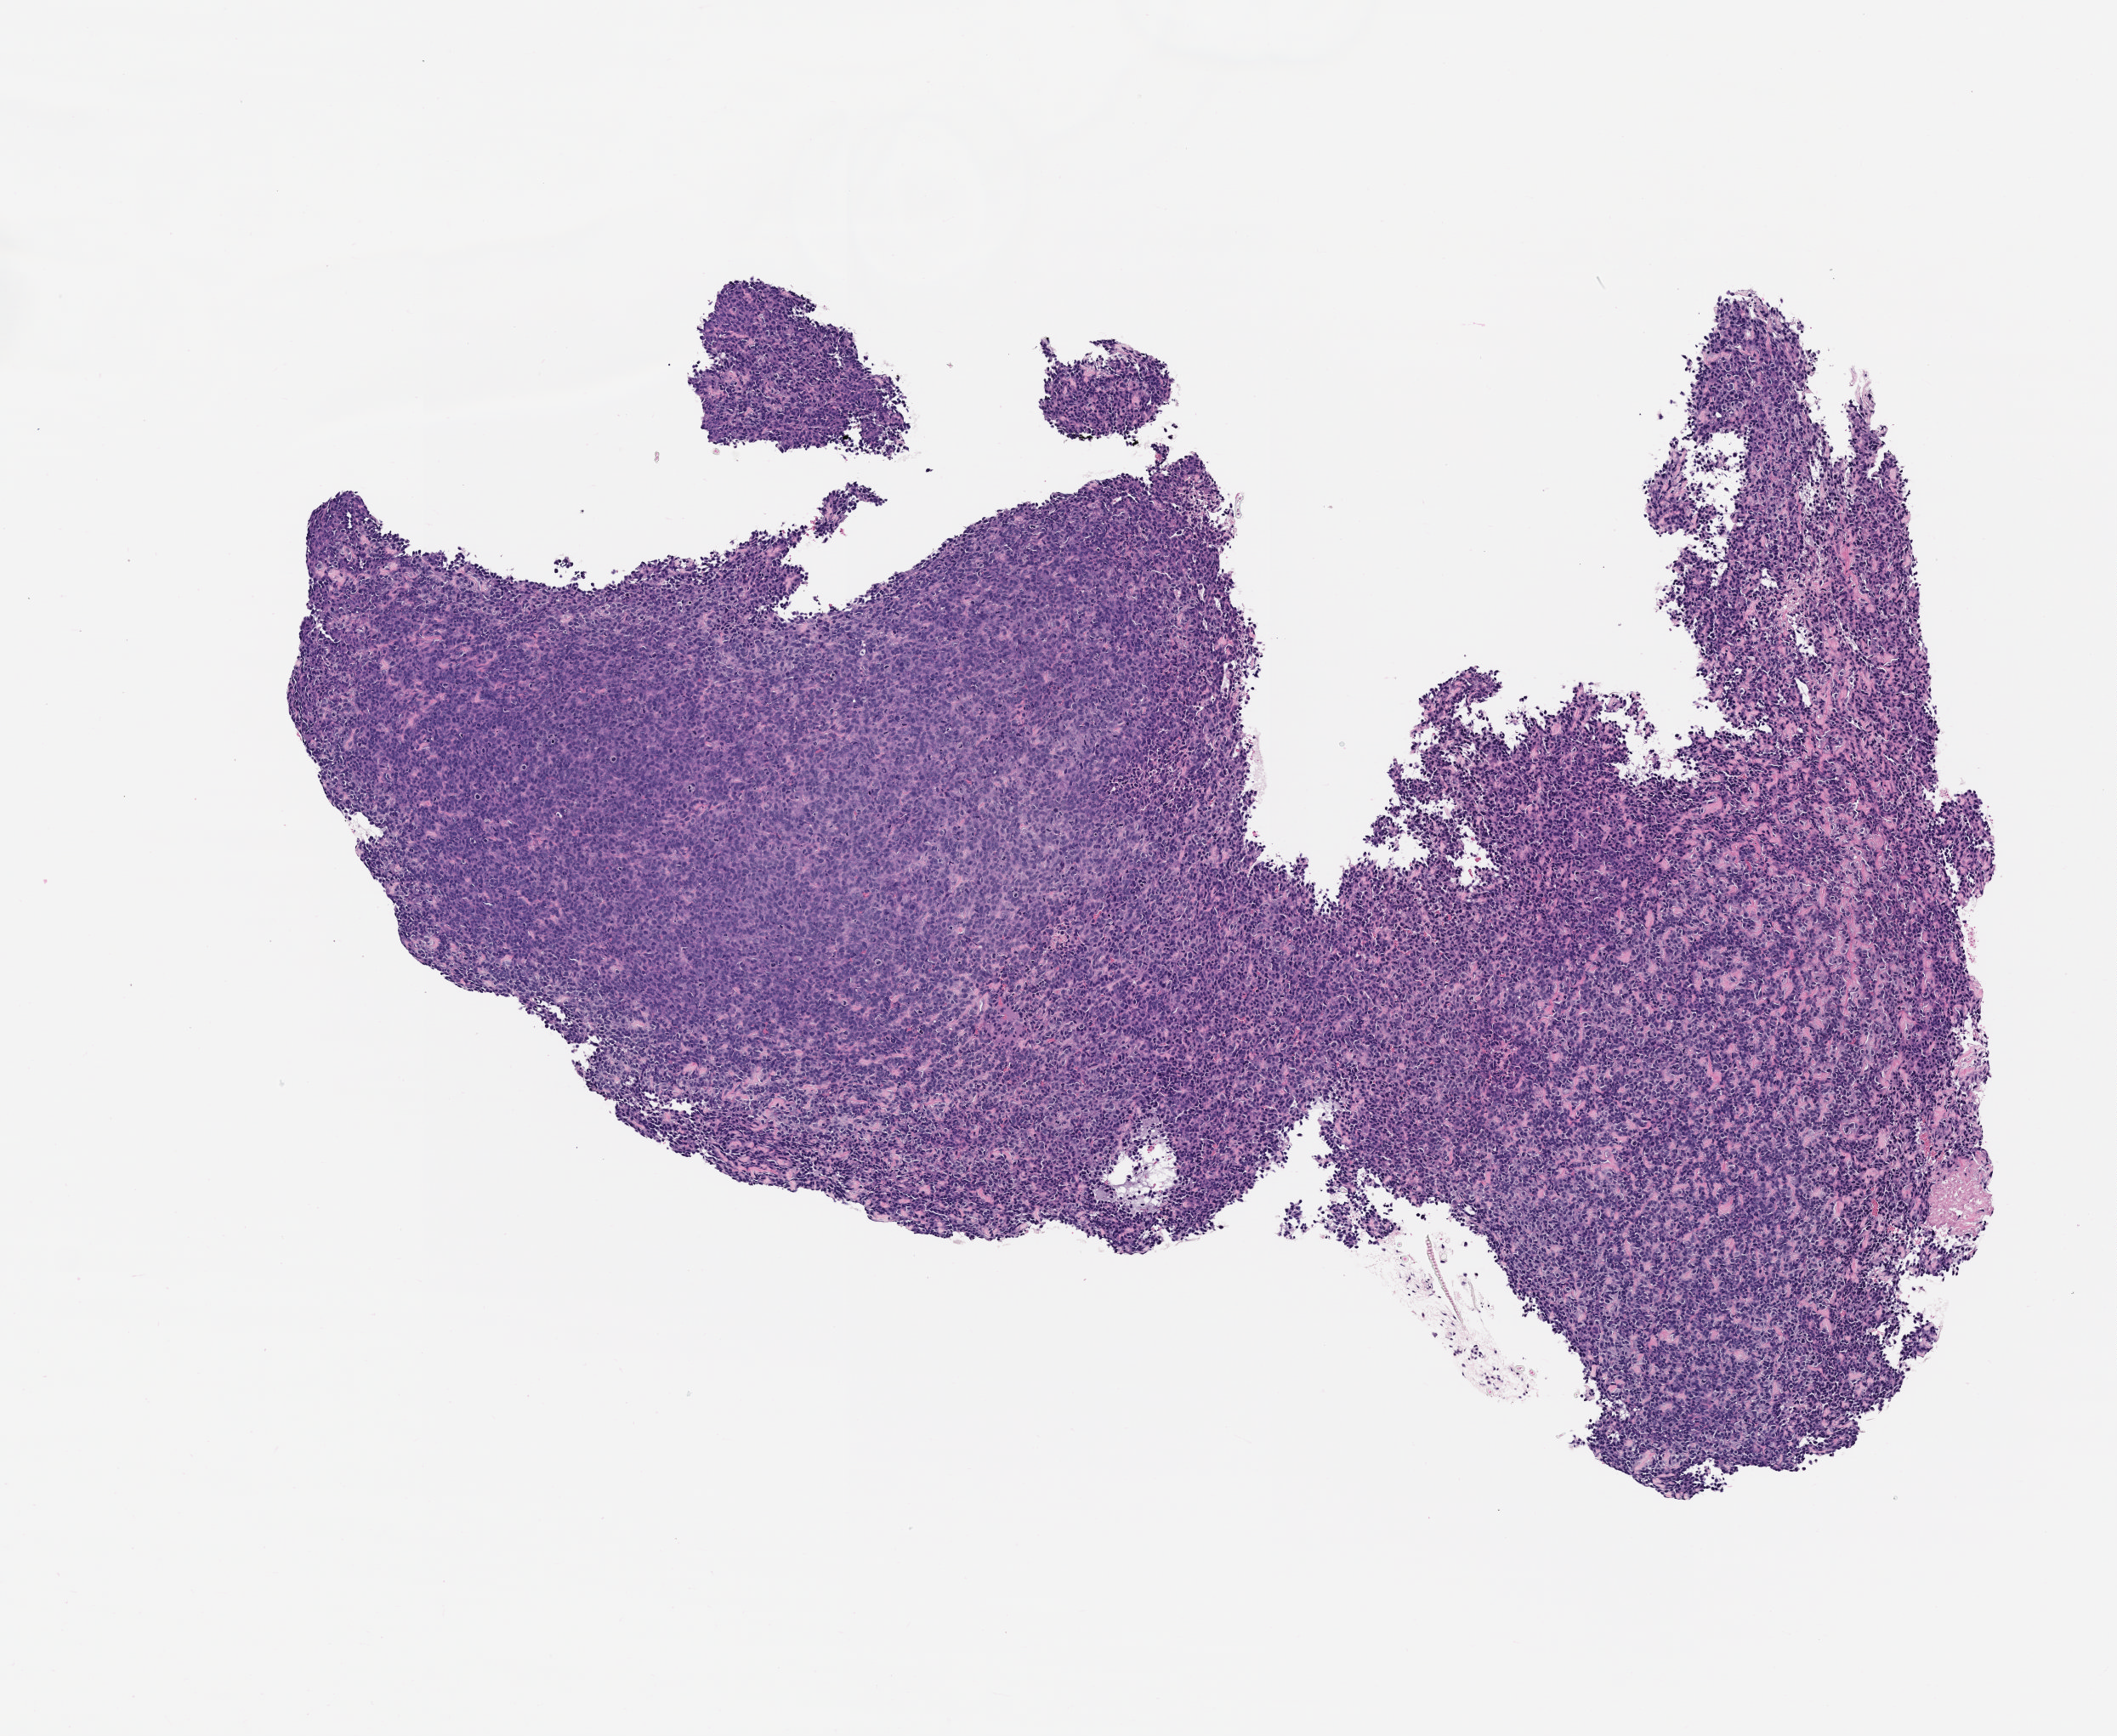
Whole-slide image, haematoxylin and eosin: patient-derived xenograft (human tumor grown in a mouse), passage 2, shown as a low-resolution overview of the whole scanned area (about 5.0 x 4.1 mm). Formalin-fixed, paraffin-embedded (FFPE) tissue. Tumor site category: bone.
- originating patient diagnosis: Osteosarcoma